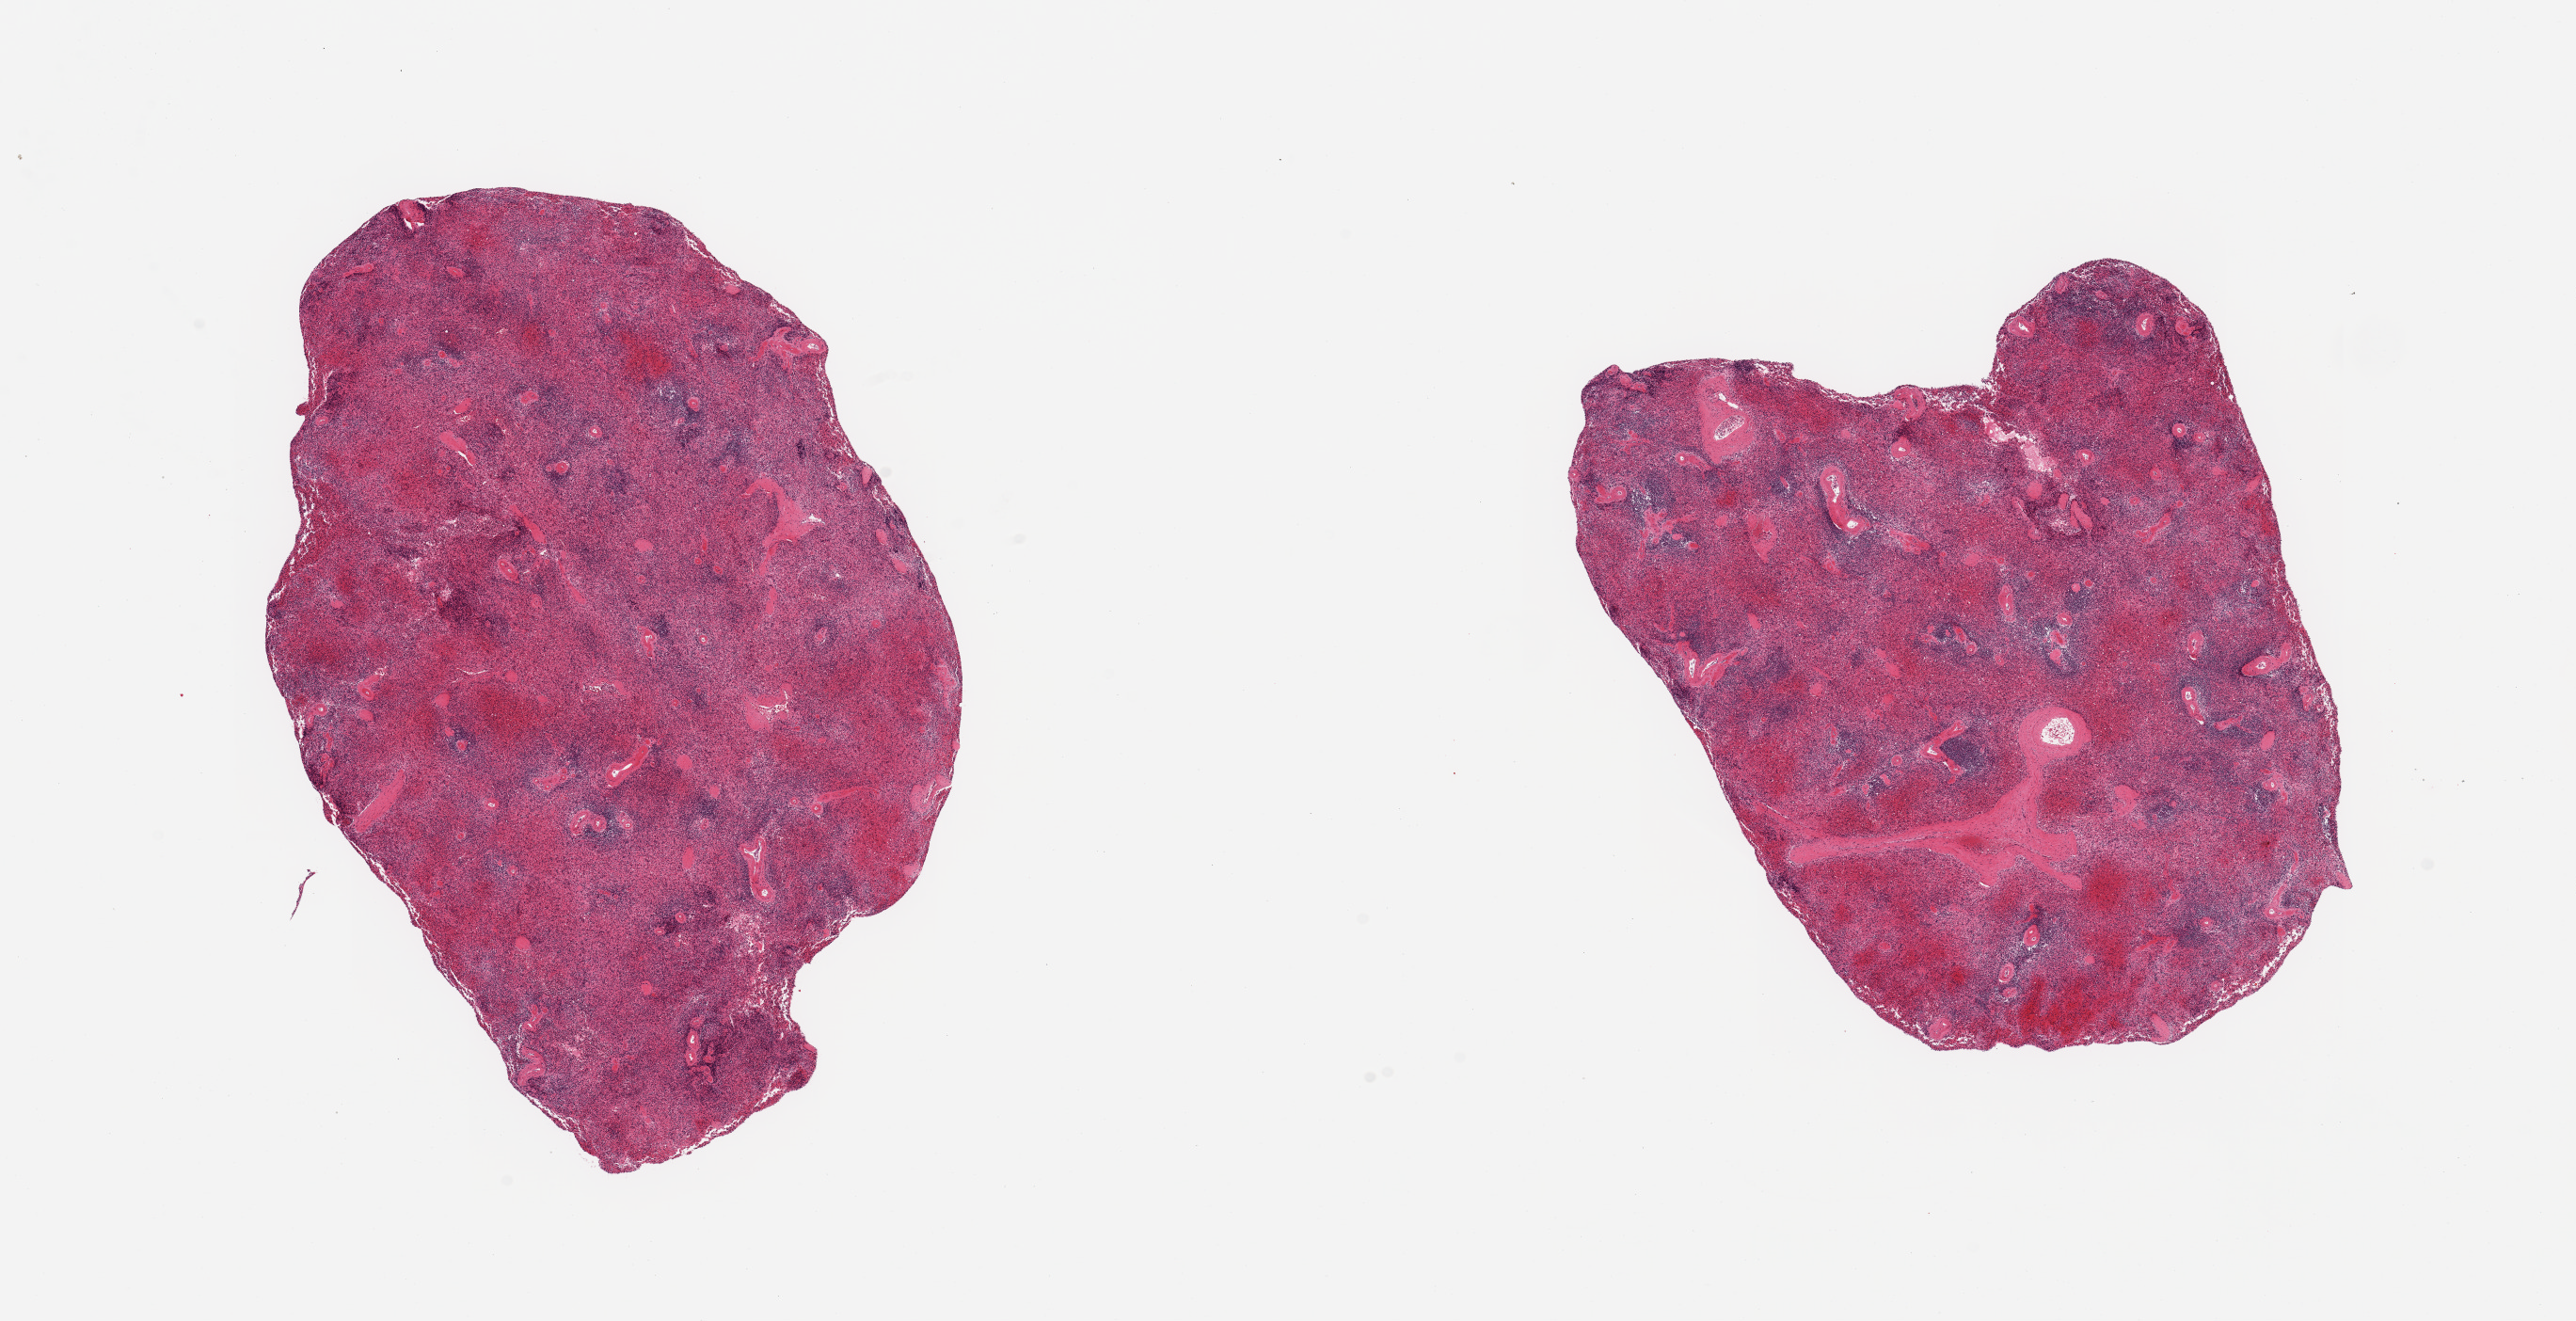
H&E whole-slide image — whole scanned area (about 21.7 x 11.1 mm, acquisition: 20x scan) shown as a low-resolution overview. PAXgene-fixed, paraffin-embedded tissue. Target tissue: spleen. Donor tissue sample. Female donor.
• reviewer comment on this tissue sample: 2 pieces; mild vascular congestioon